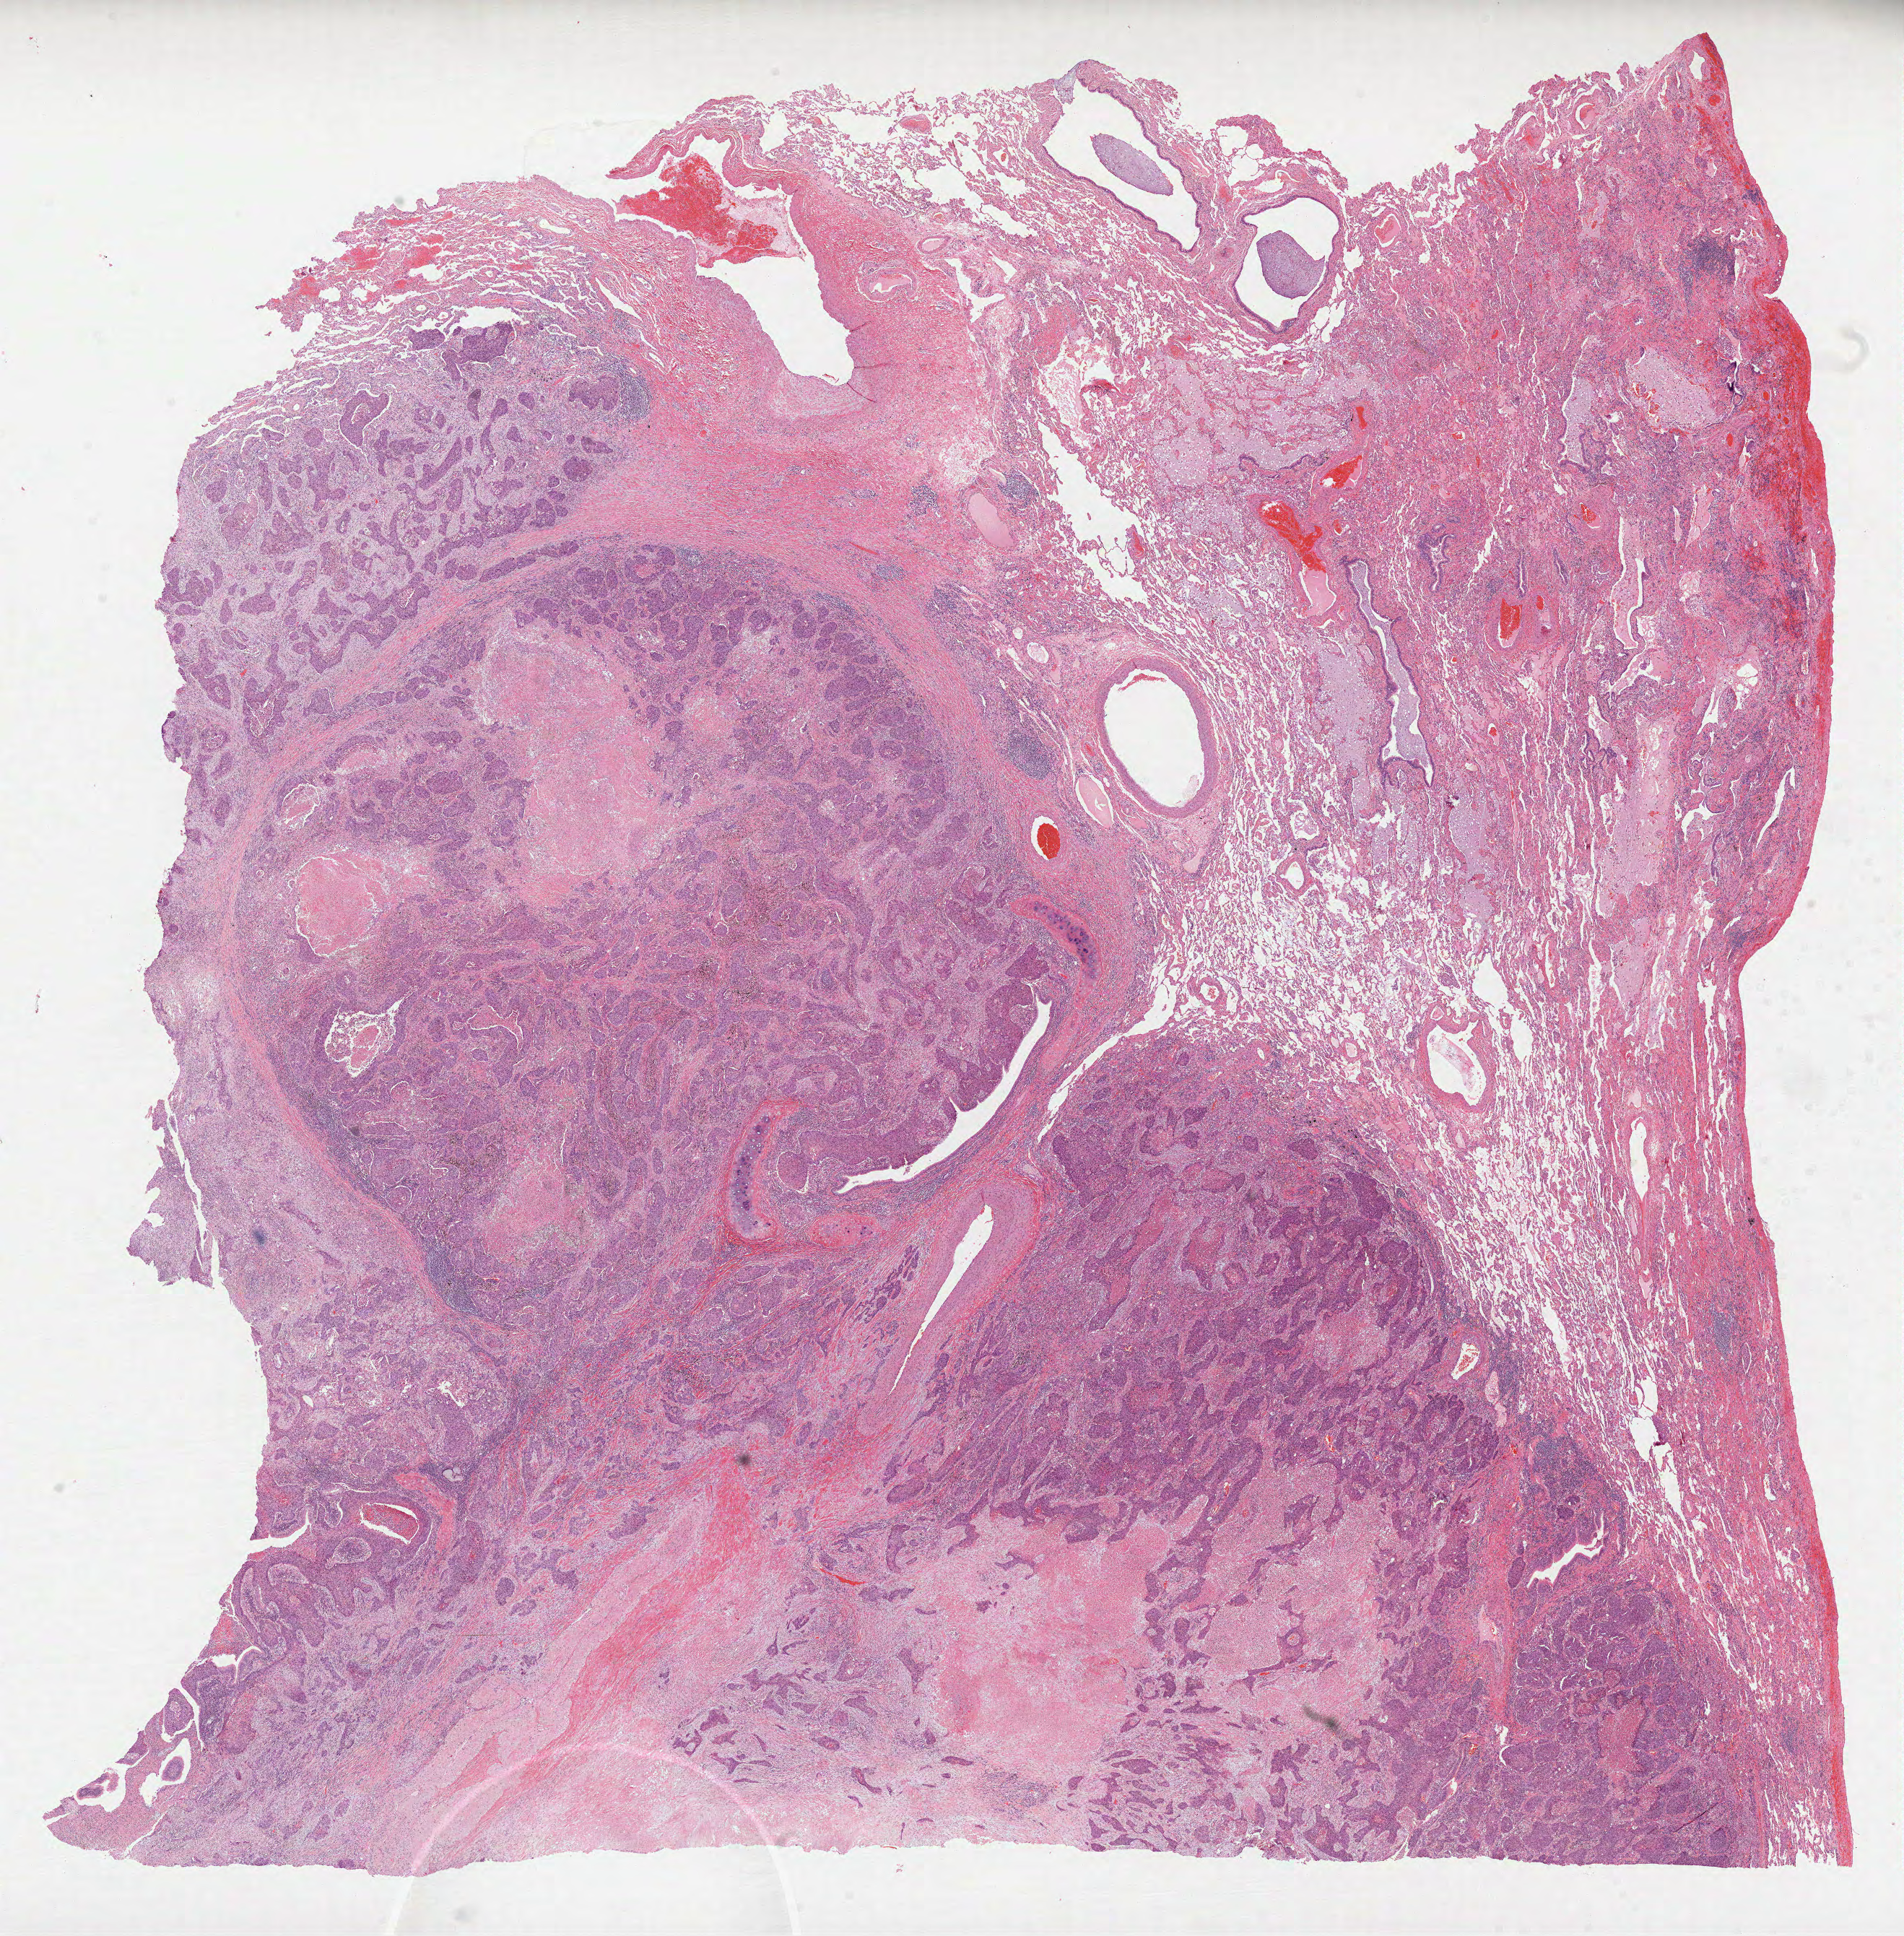
Whole-slide histology image, H&E-stained, shown as a low-resolution overview of the whole scanned area (about 21.3 x 21.6 mm), formalin-fixed paraffin-embedded (FFPE) diagnostic section, lung, primary tumour sample. Male patient; age at initial diagnosis 73 years.
Pathologic diagnosis: Squamous cell carcinoma, NOS (upper lobe, lung).